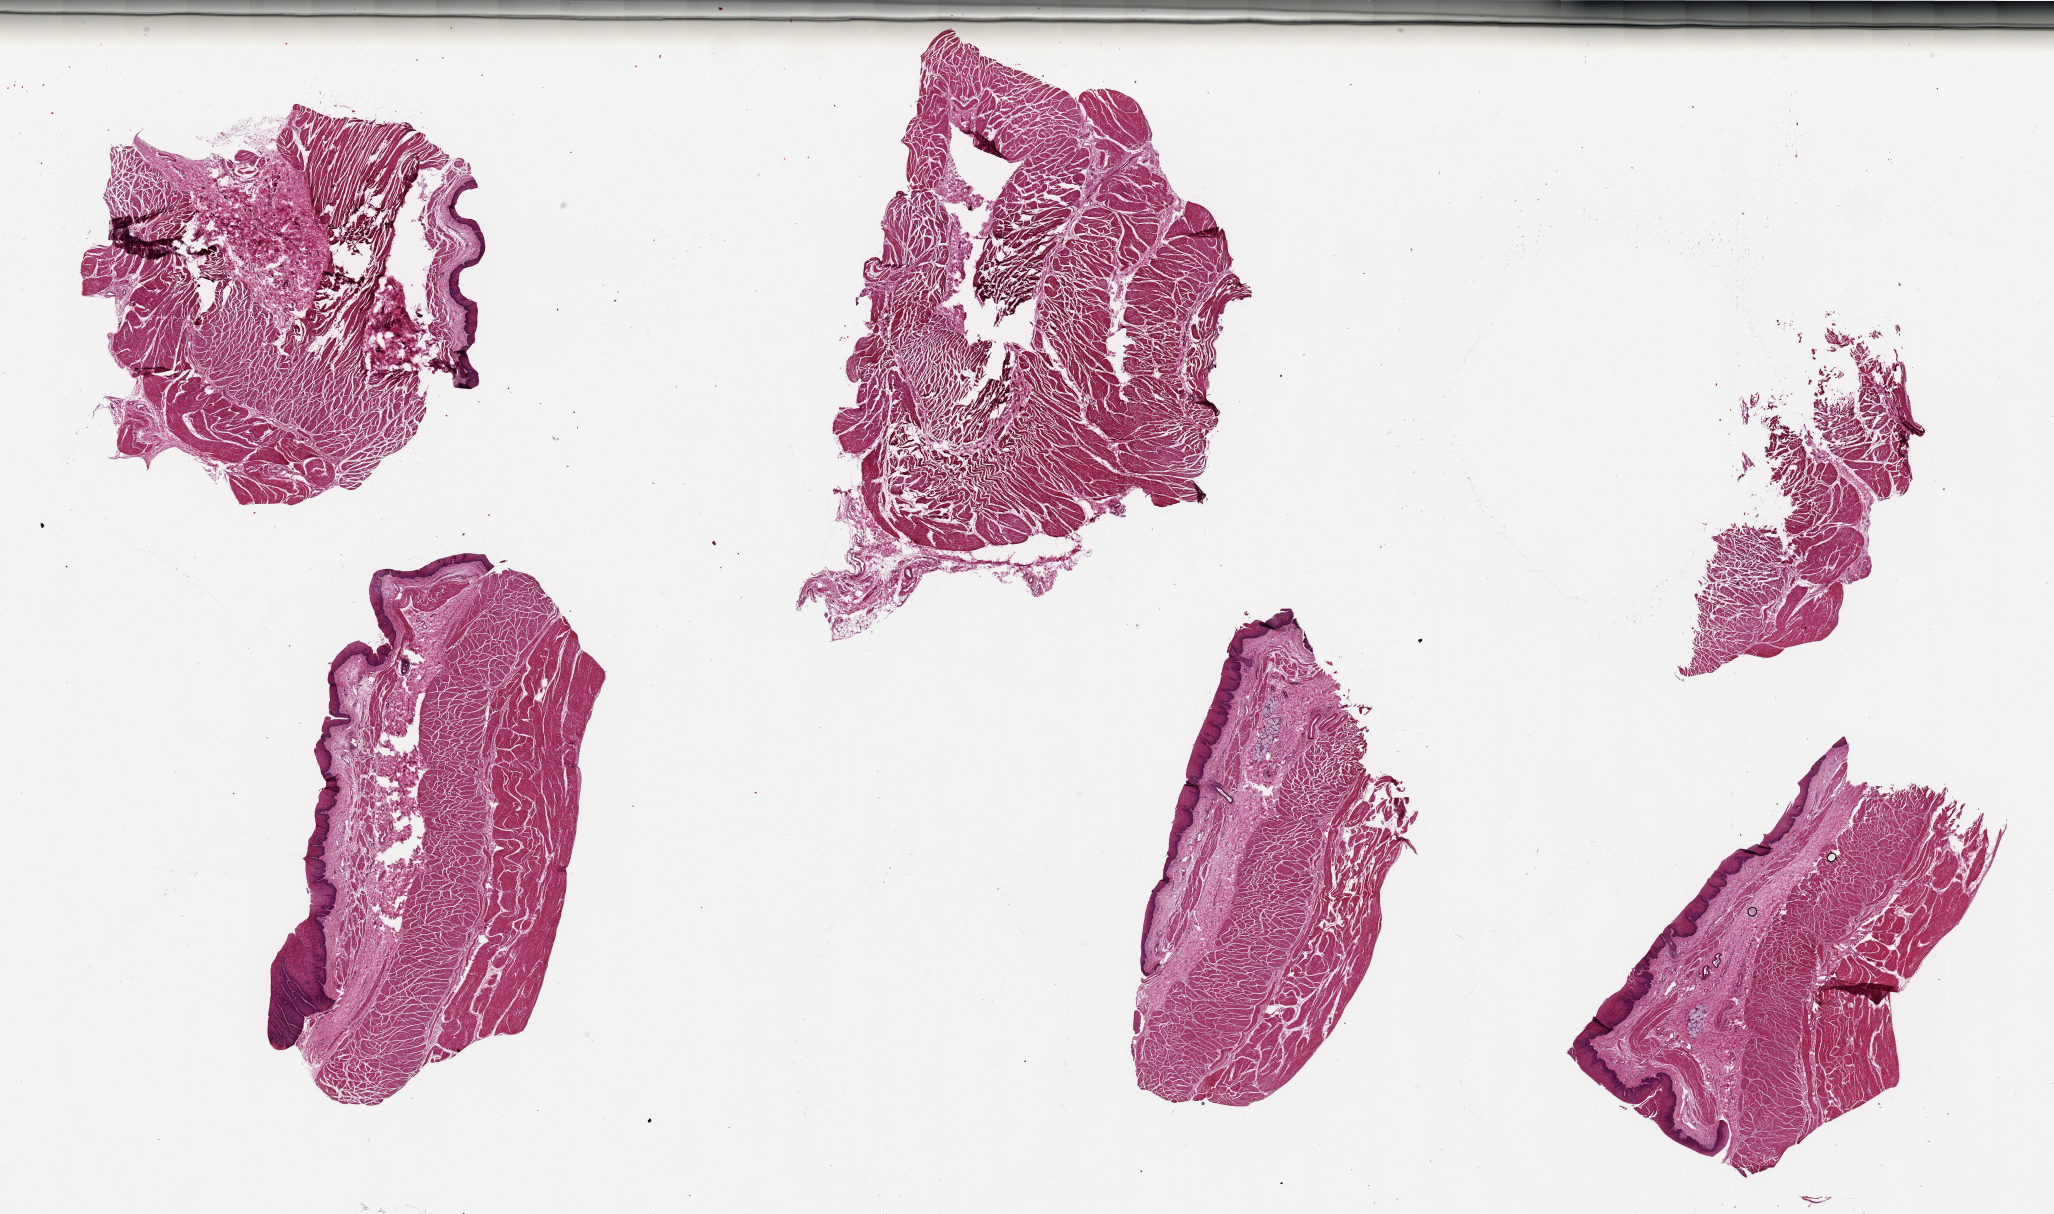
Haematoxylin and eosin whole-slide image — a low-resolution overview of the entire scanned area, about 32.5 x 19.2 mm (from a 20x scan), PAXgene-fixed paraffin-embedded (PFPE) section, target tissue: esophageal muscle, tissue donor sample. Donor: male.
* reviewer comment on this tissue sample: 6 pieces, With 5-10% adherent squamous mucosa